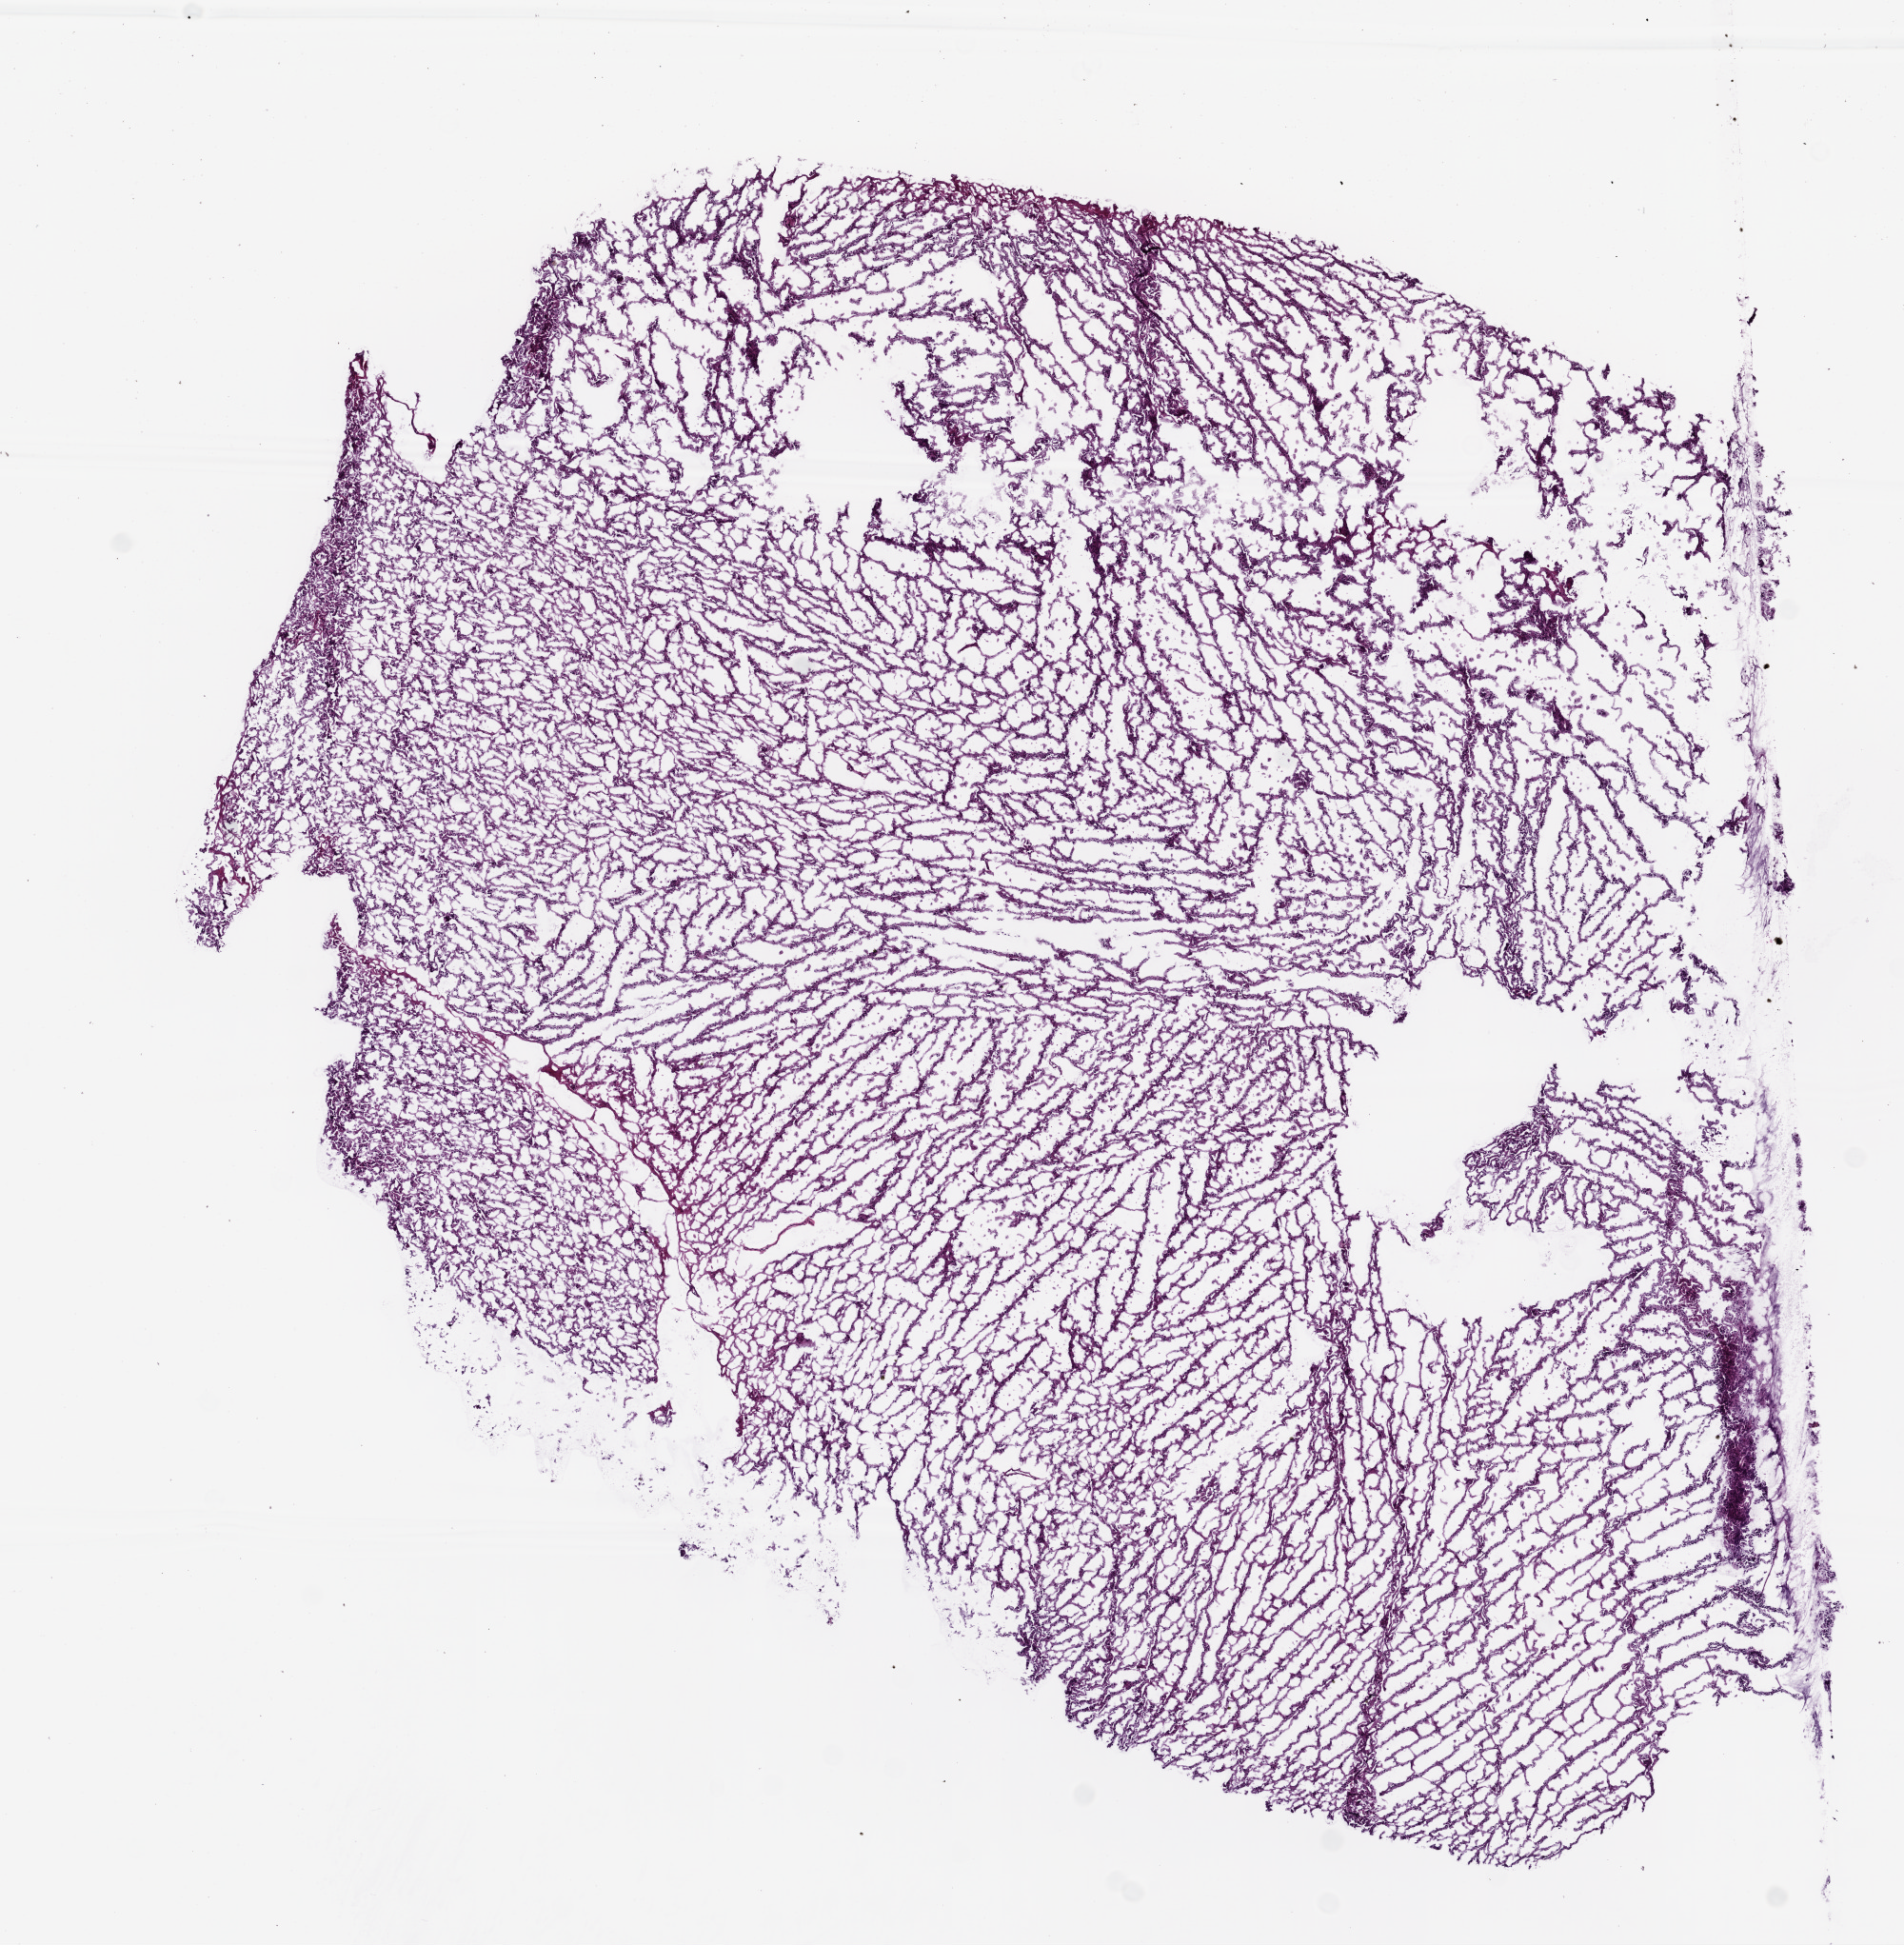
Hematoxylin and eosin (H&E) stained whole-slide image — a low-resolution overview of the entire scanned area, about 8.0 x 8.2 mm; frozen section from the bottom of the tissue portion; primary tumour sample from the brain. Patient: female, age at initial diagnosis 56 years.
Histologic diagnosis: Oligodendroglioma, anaplastic.